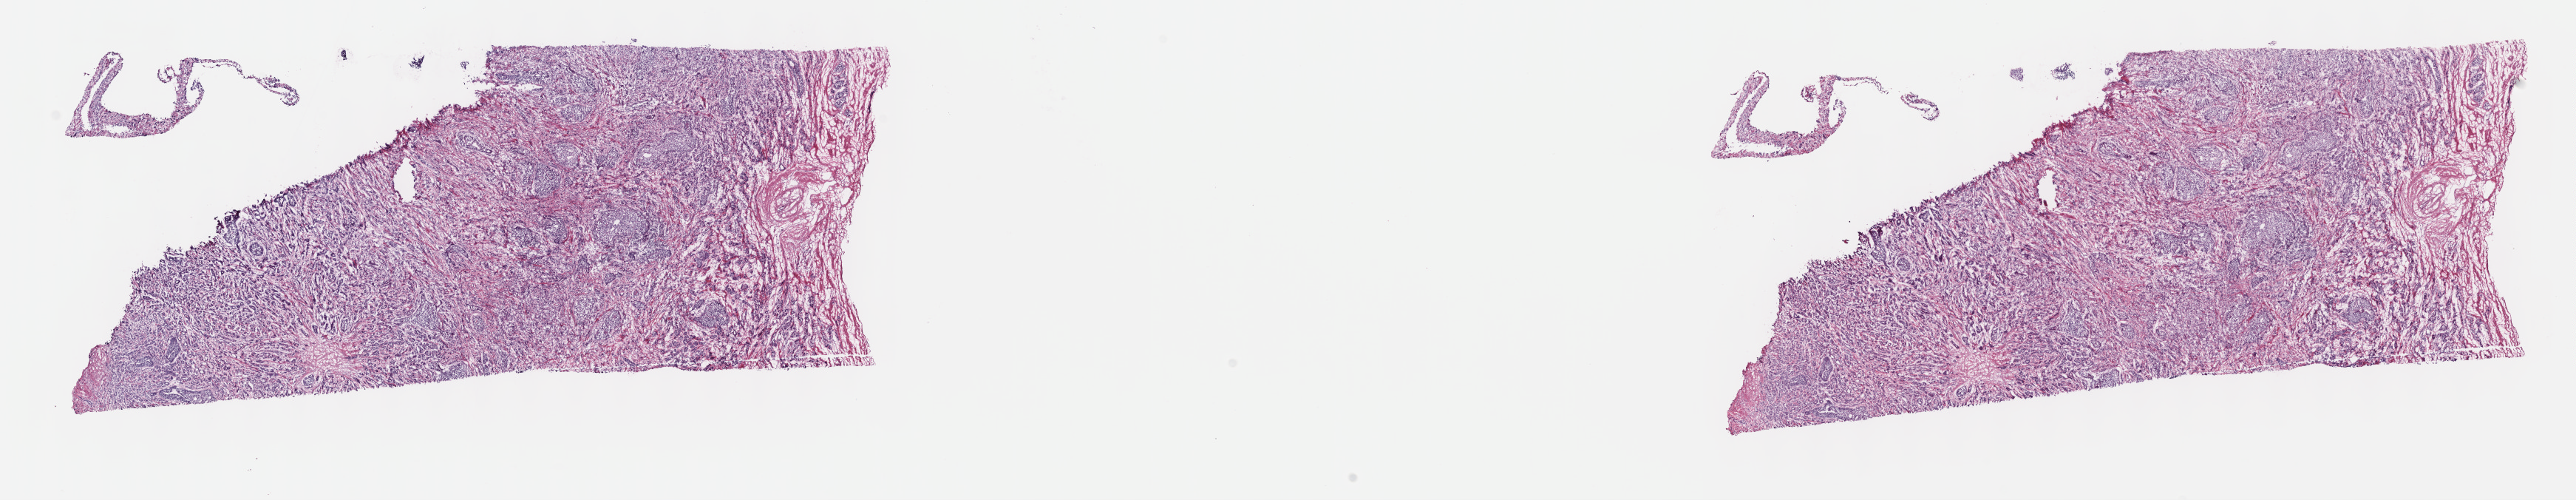
Whole-slide histology image, H&E, shown as a low-resolution overview of the whole scanned area (about 28.2 x 5.5 mm, from a 40x scan), frozen section from the top of the tissue portion, prostate, primary tumour sample. Male, age 64 years at initial diagnosis. Gleason score: 9 (4+5). Slide review estimates, as recorded: tumour cells 80%, tumour nuclei 80%, normal cells 0%, stromal cells 20%, necrosis 0%. Inflammatory infiltration, as recorded: lymphocyte infiltration 40%, monocyte infiltration 20%, neutrophil infiltration 20%.
Lymph nodes positive (case pathology): 3 of 29 examined. Diagnosis: Infiltrating duct carcinoma, NOS (prostate gland).